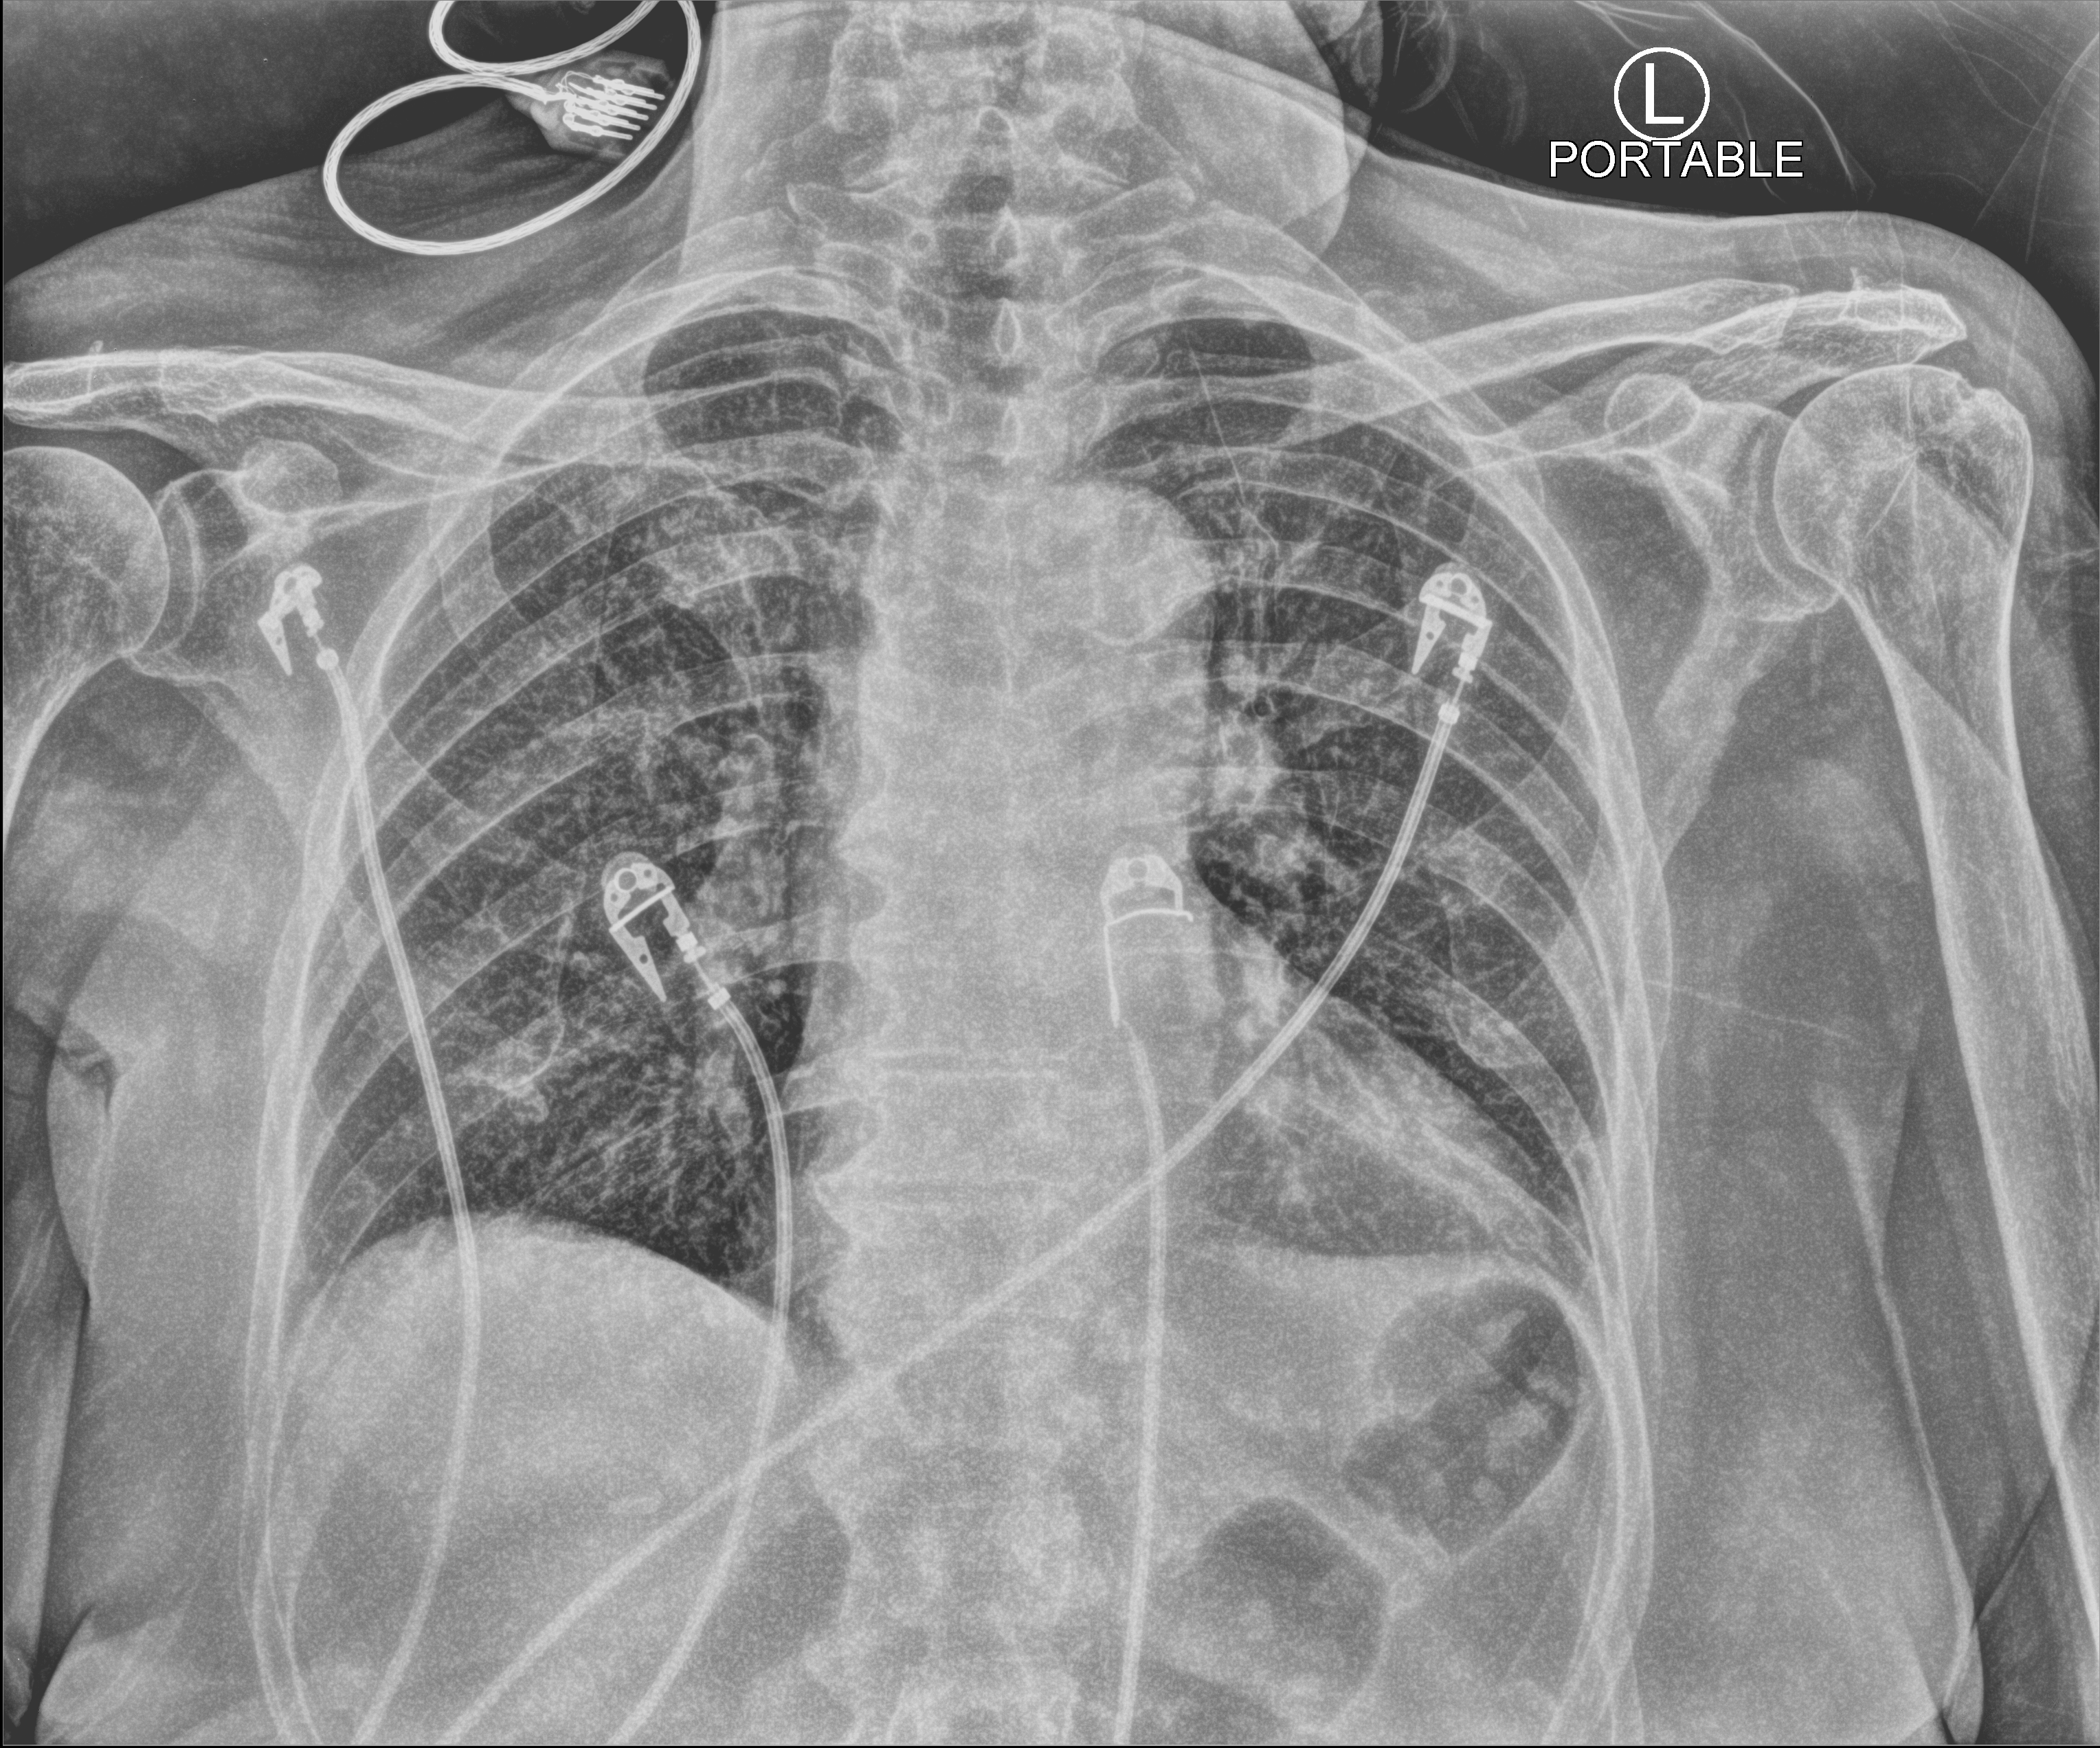
Chest X-ray (portable), anteroposterior (AP) projection. Patient hospitalised with COVID-19; female, aged 75–90 years.
Hospital-stay facts (about this admission, not read from this image; timing relative to this image not recorded): mechanically ventilated during this hospital stay: no; hypertension (admission record): no.